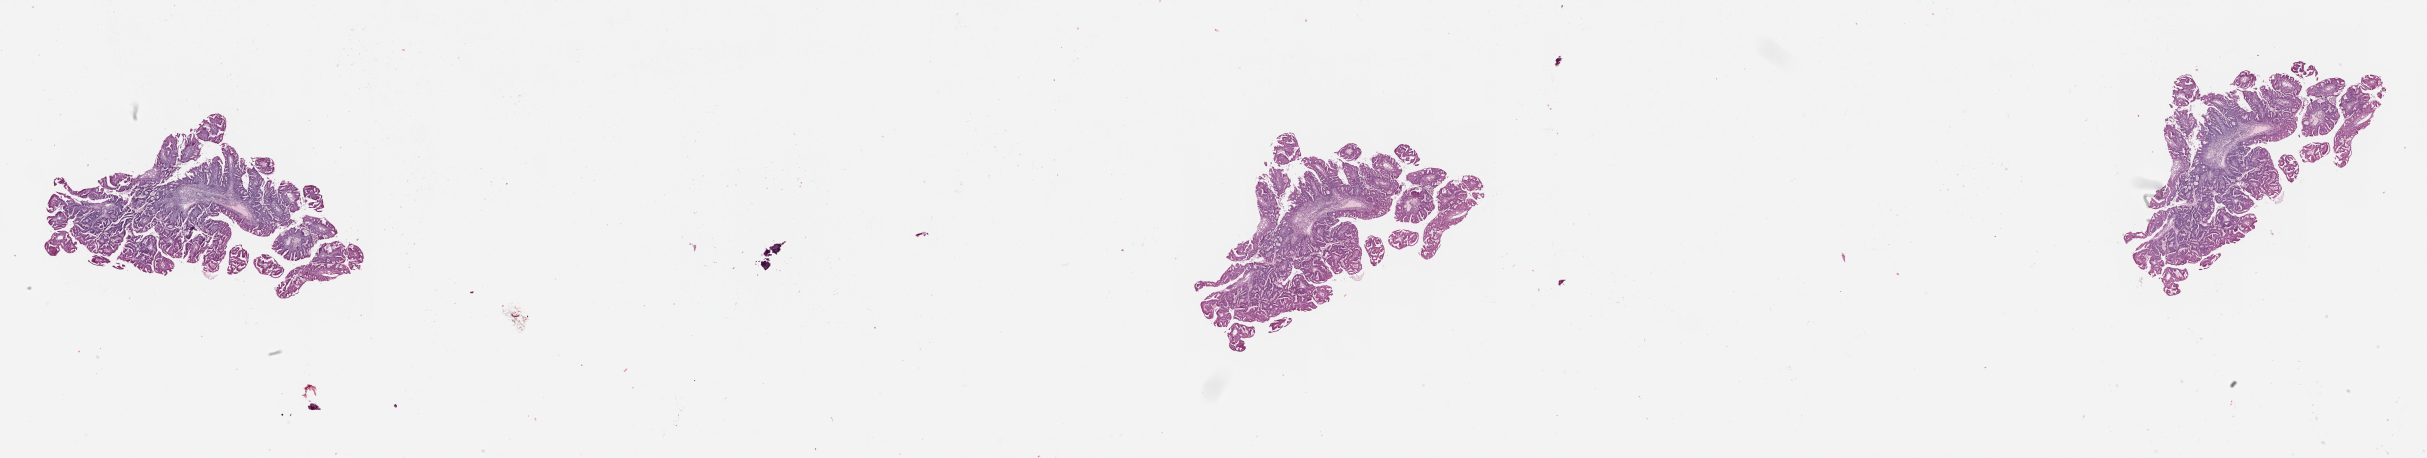
H&E-stained whole-slide image, whole scanned area (about 39.1 x 7.4 mm, acquisition: 20x scan) shown as a low-resolution overview; tumour tissue sample, sampled site: uterus. 67-year-old female patient. Histologic grade: G1 (well differentiated). Pathologist review of this section (percent, as recorded): tumour nuclei 80%, necrosis 0%.
Primary tumour site (as recorded): posterior endometrium. AJCC pathologic stage: I. Diagnosis: Endometrioid adenocarcinoma, NOS.